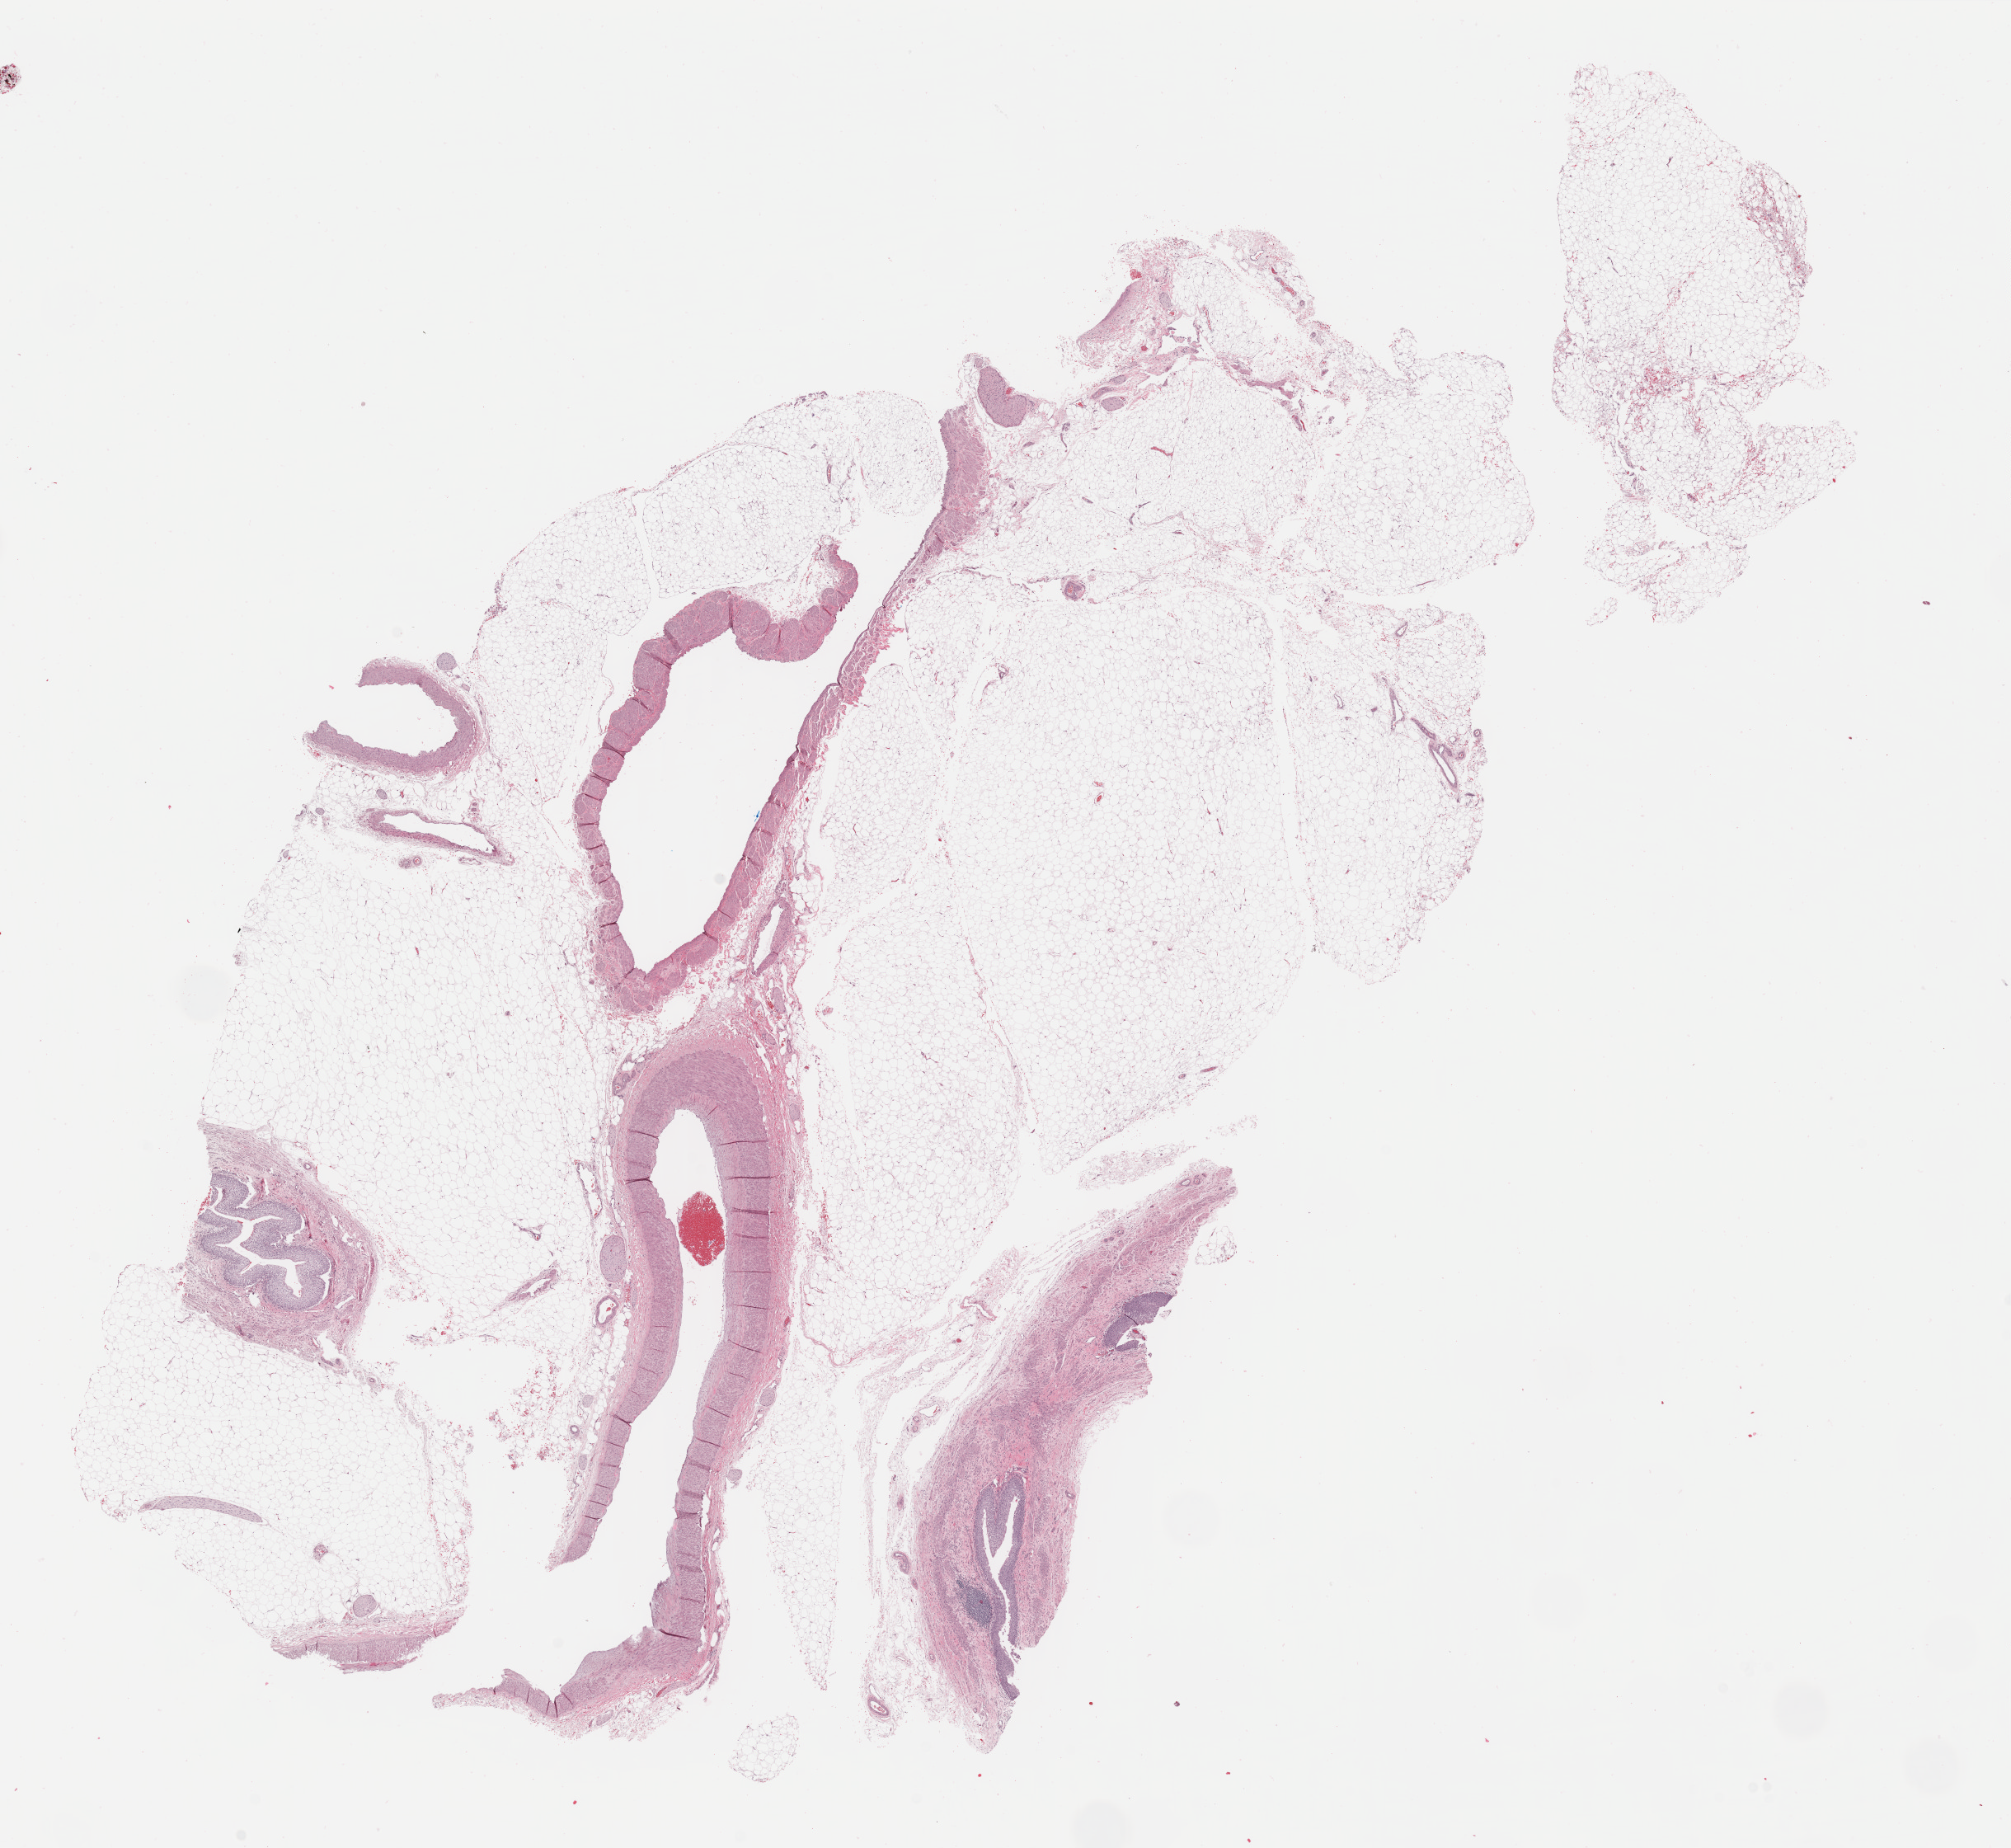
Whole-slide histology image, H&E-stained, whole scanned area (about 19.3 x 17.7 mm, acquisition: 40x scan) shown as a low-resolution overview; FFPE section; solid tissue normal (non-tumour tissue) sample from the kidney. Female, age 57 years at initial diagnosis. Slide review estimates, as recorded: tumour cells 0%, tumour nuclei 0%, normal cells 100%, stromal cells 0%, necrosis 0%. Inflammatory infiltration, as recorded: lymphocyte infiltration 0%, monocyte infiltration 0%, neutrophil infiltration 0%.
This section: solid tissue normal (non-tumour) sample from the same patient. Patient diagnosis: Renal cell carcinoma, chromophobe type.